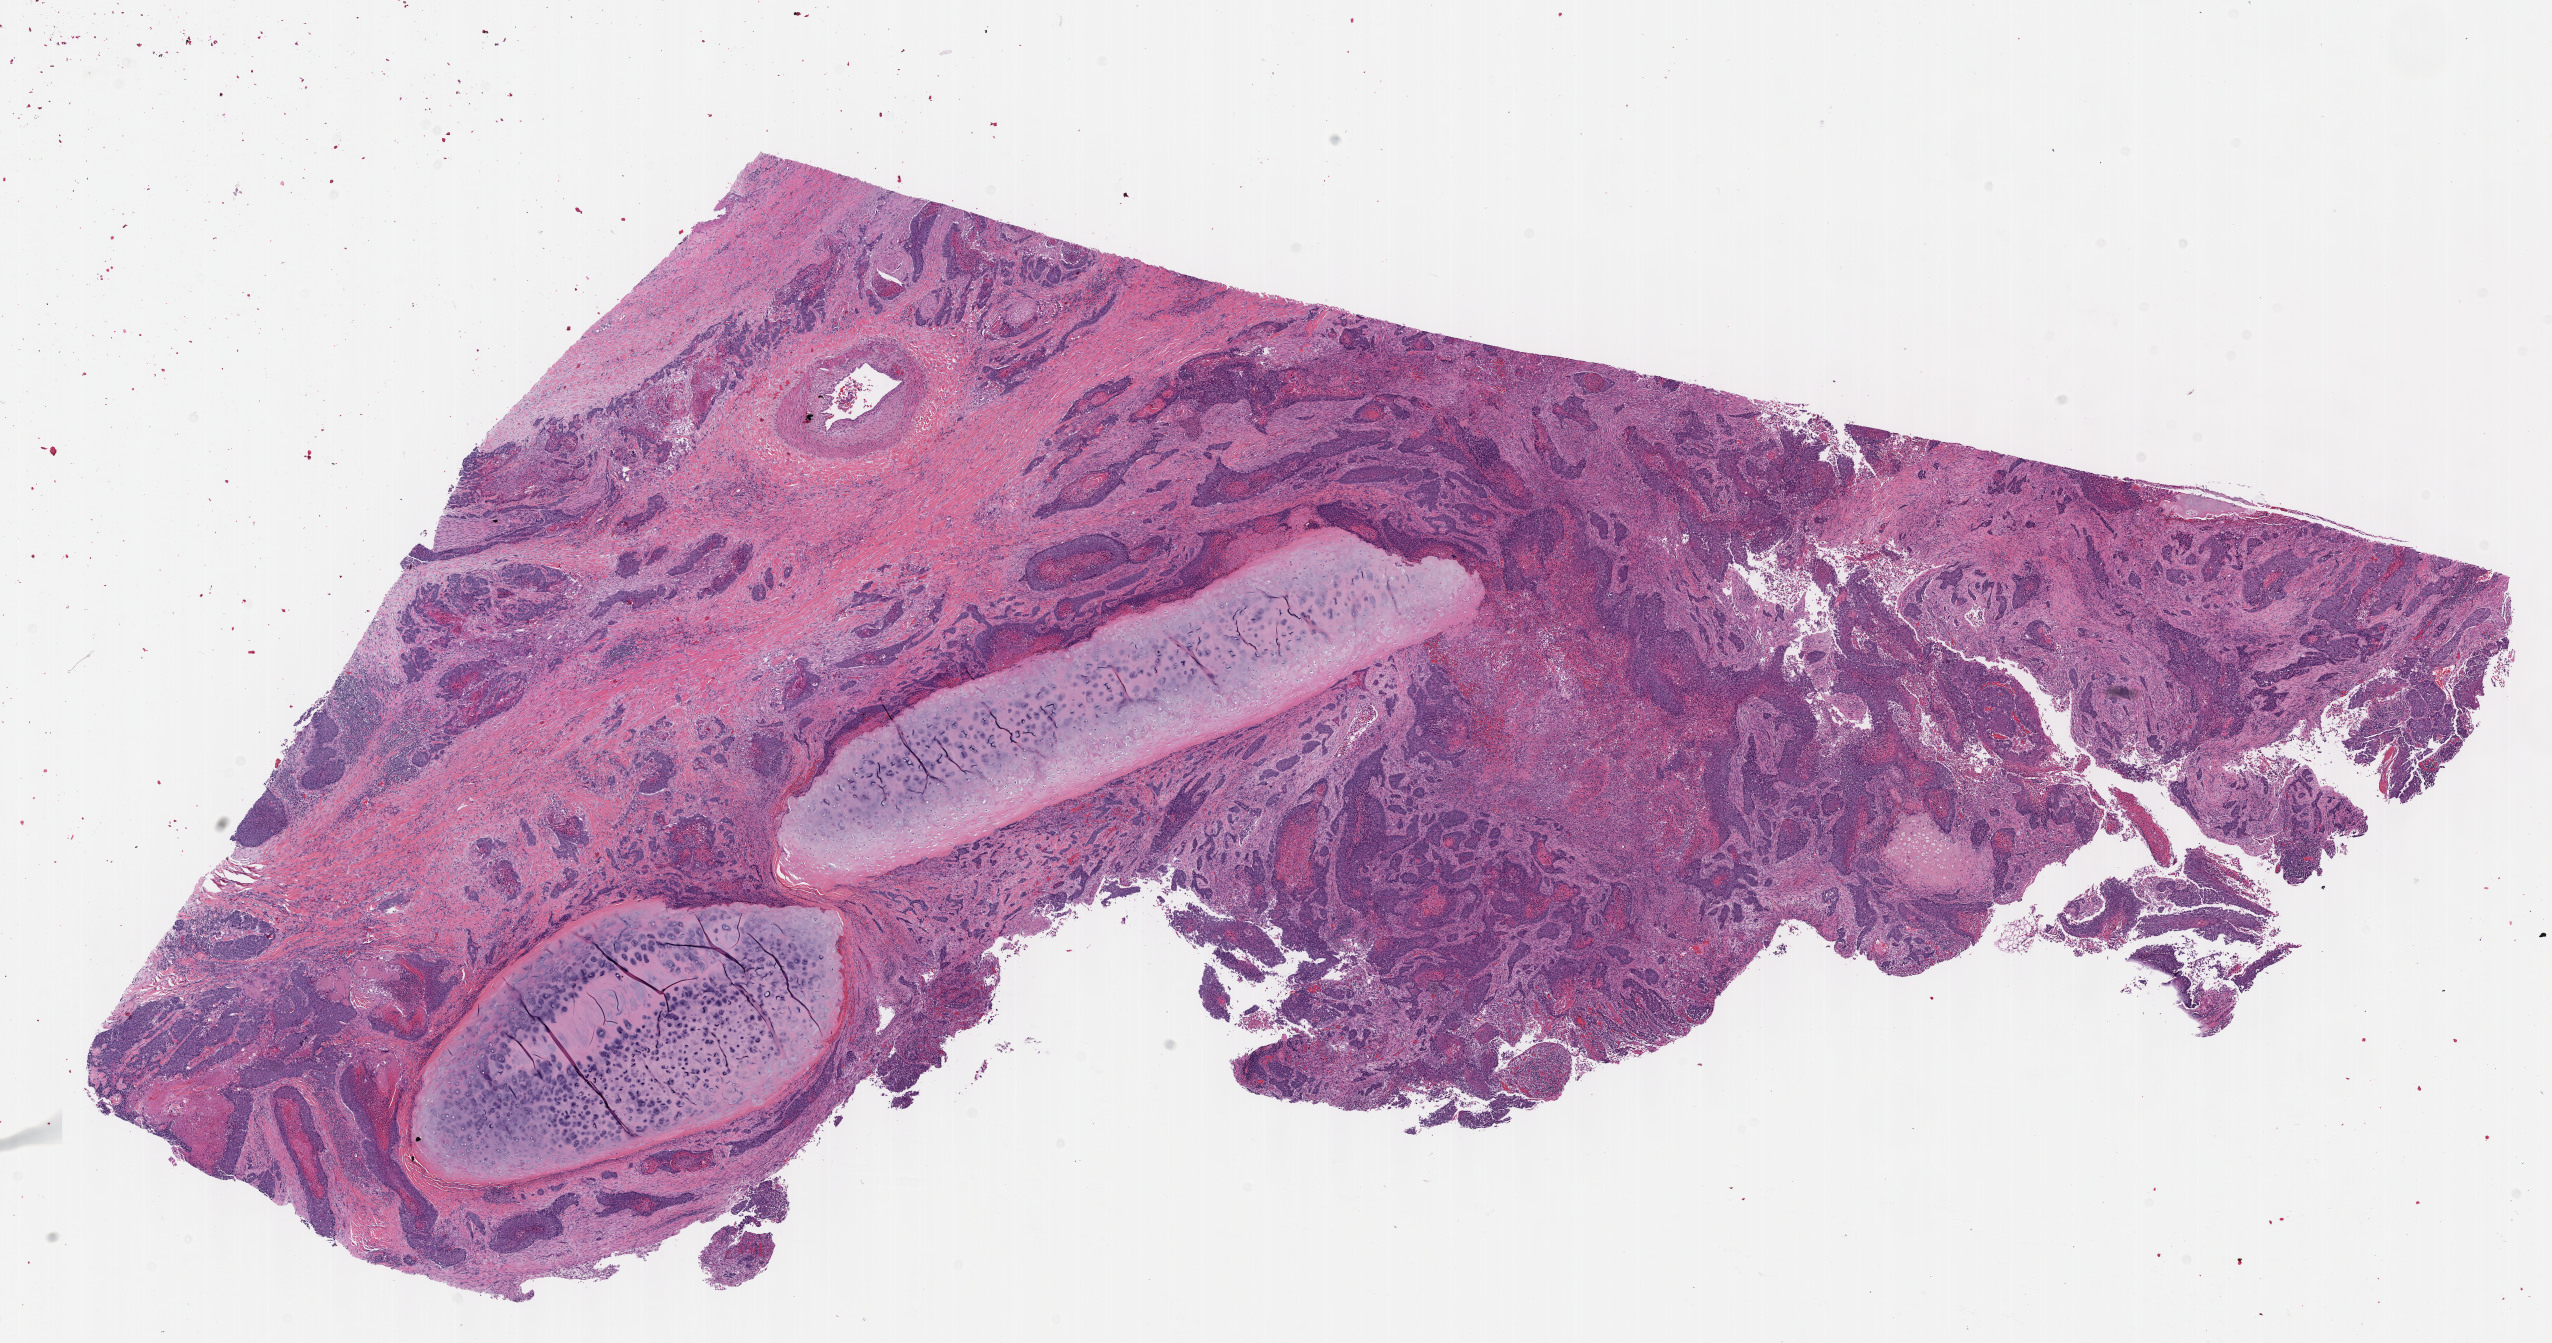
Digitized Hematoxylin and eosin (H&E) stained tissue section (whole slide), low-resolution overview of the scanned area, about 20.6 x 10.9 mm (from a 40x scan); formalin-fixed paraffin-embedded (FFPE) diagnostic section; sample: primary tumour, lung. Male patient; age at initial diagnosis 59 years.
- histologic diagnosis: Squamous cell carcinoma, NOS (middle lobe, lung)
- AJCC pathologic stage: IIIB (7th edition)